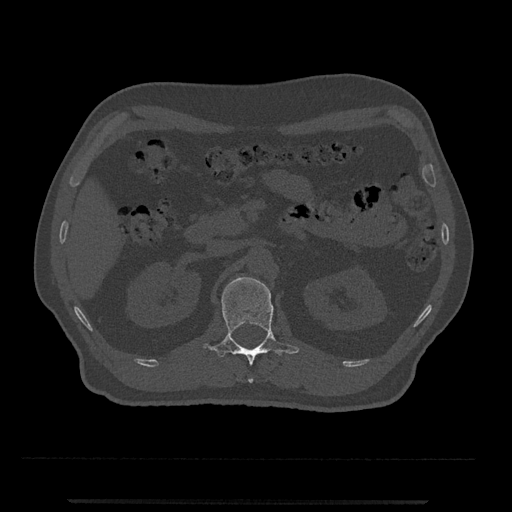
CT including the spine, one axial slice; position 335 of 797 along the scan axis; reconstruction kernel Br40s/3; 120 kVp; bone window (W 1800 / L 400 HU); 512 × 512 image matrix, field of view 419 × 419 mm. Male patient, age 63 years. Case-level facts recorded for this patient, not image findings: primary cancer: prostate.
Structures marked on this image (semi-automatically segmented with operator editing):
- L1 vertebra: bounding box <203,277,299,383> (left, top, right, bottom; pixels)